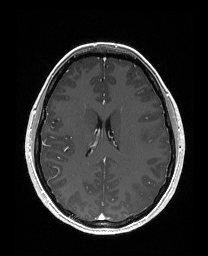
Brain MRI from a brain-tumour surgery series, one axial slice; slice 99 of 176 in the series (ordered by position); T1-weighted post-contrast; 1 mm slice thickness; 208 × 256 image matrix. From the clinical record (not read from this slice): histopathology: Astrocytoma; WHO grade: 3; IDH mutation: yes.
Annotated regions visible in this slice (outlined manually by an expert reader):
- tumour: box from (x=138, y=129) to (x=151, y=143) px